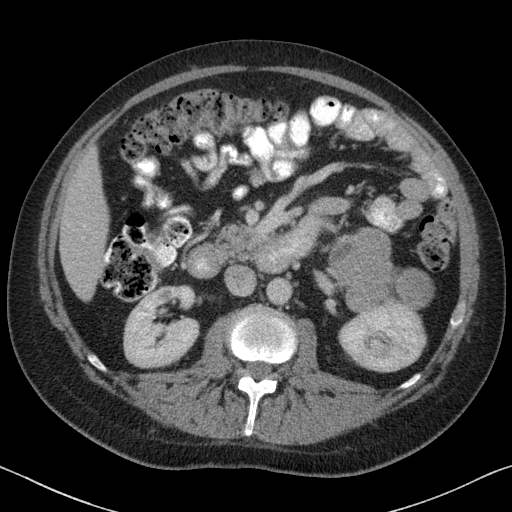
Contrast-enhanced abdominal CT, one axial slice; position 33 of 88 along the scan axis; reconstruction kernel B31f; soft-tissue window (W 400 / L 40 HU); 3 mm slice thickness; 512 × 512 image matrix. Patient: male, 51 years. From the clinical record (not read from this slice): diagnosis: adrenocortical carcinoma; tumour side: left adrenal; tumour size at pathology: 16.5 cm; Ki-67 index: 30 %; stage (as recorded): 2.
Structures marked on this image (semi-automatically segmented with operator editing):
- mass: box from (x=329, y=228) to (x=431, y=312) px